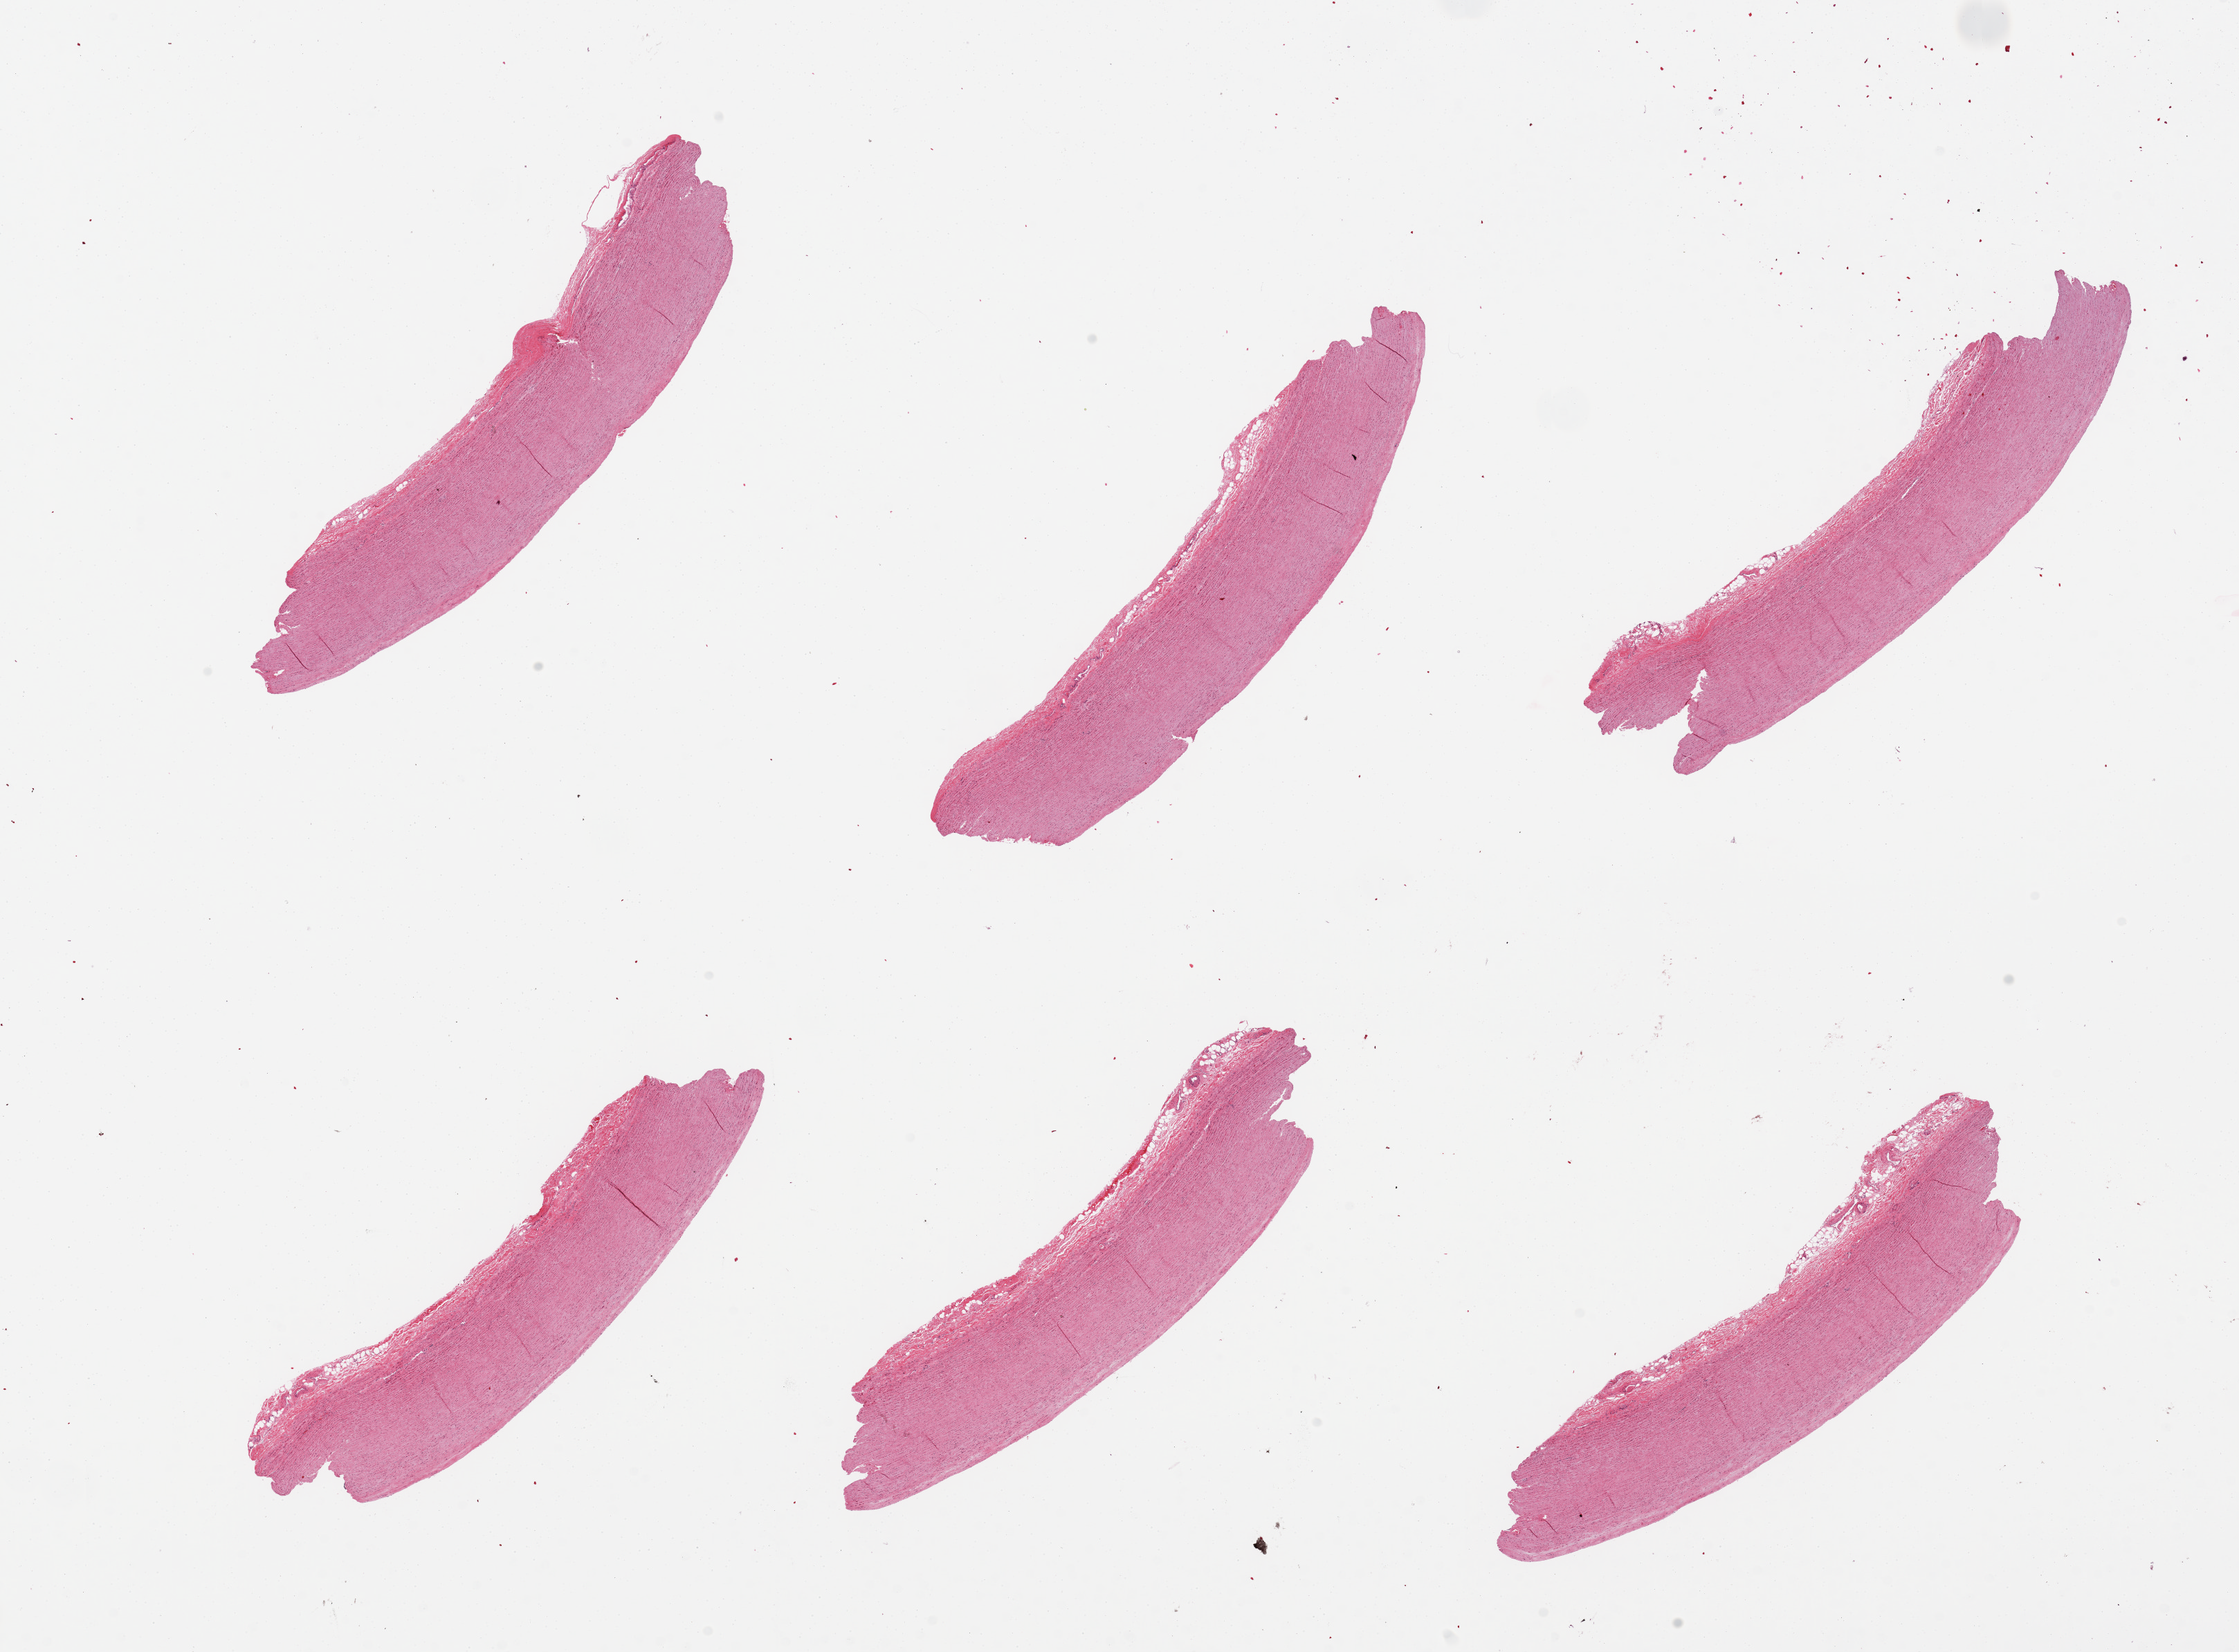
Digitized hematoxylin and eosin (H&E)-stained section, brightfield — shown as a low-resolution overview of the whole scanned area (about 25.6 x 18.9 mm). PAXgene-fixed, paraffin-embedded tissue. Sampled site (target tissue): aorta. Donor tissue sample. Male donor.
Pathologist's review note for this sample: 6 pieces; minimal plaques, well trimmed.